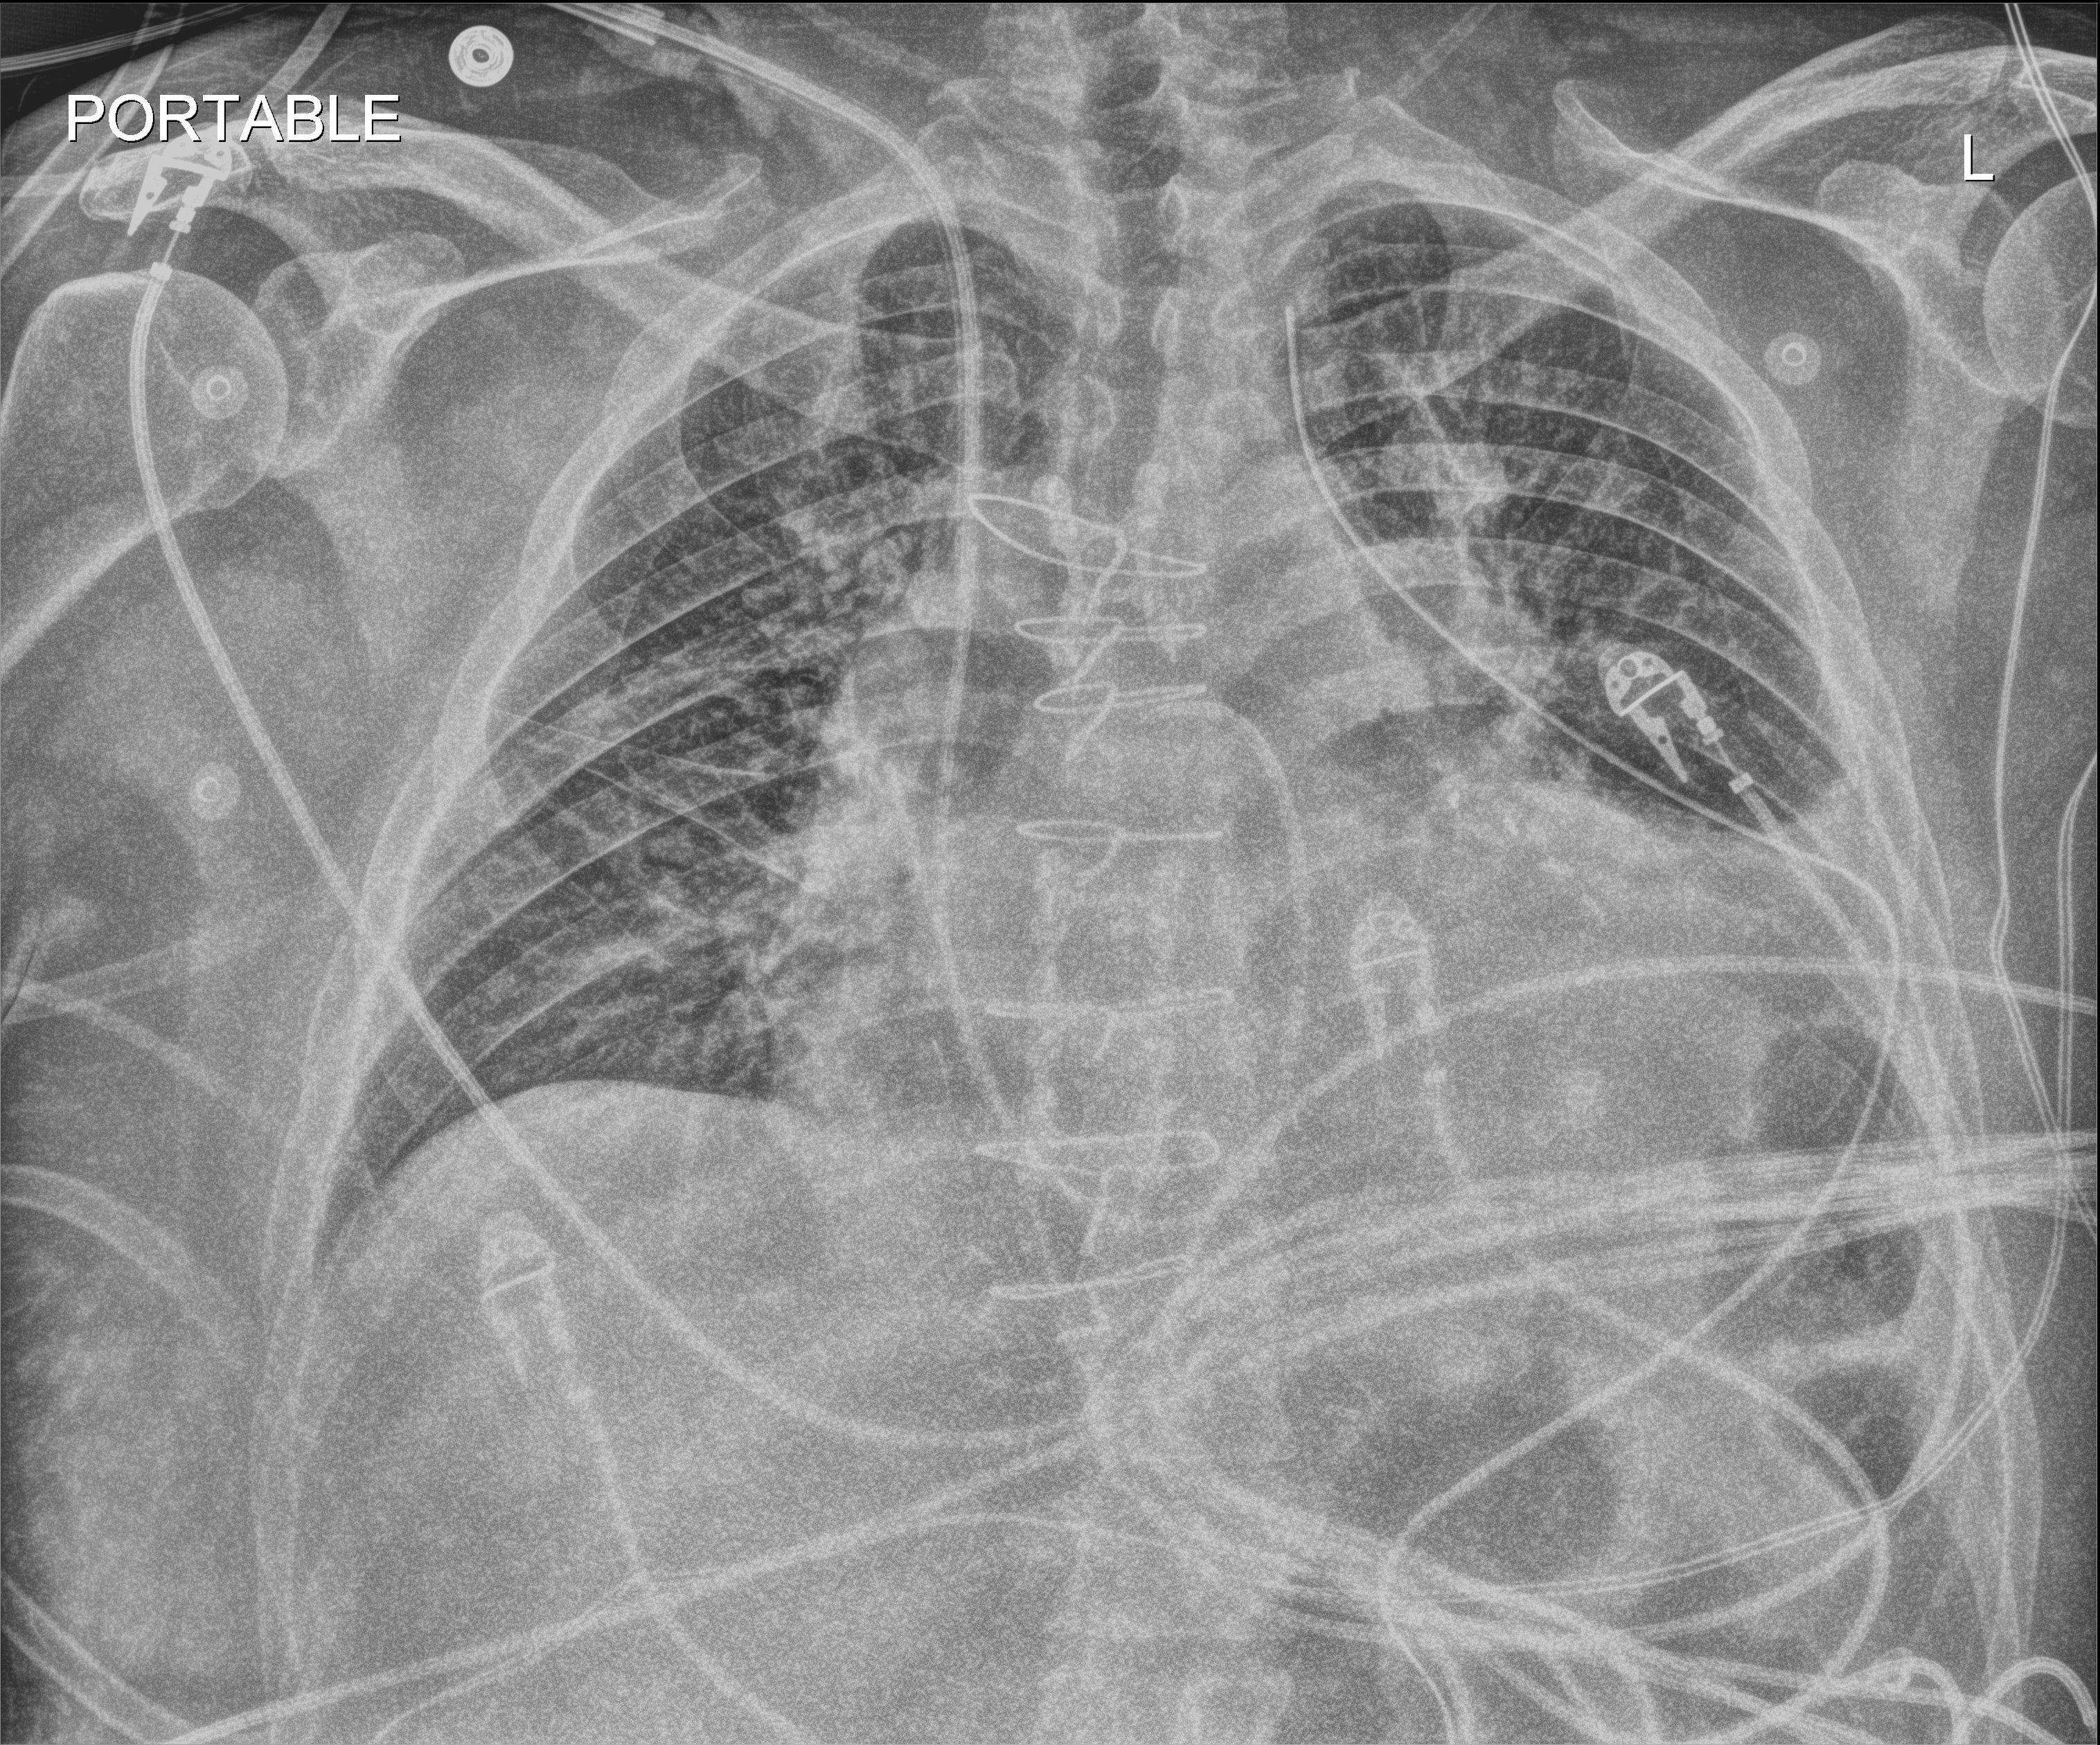
Bedside chest radiograph (digital radiography); anteroposterior (AP) projection. Male patient hospitalised with COVID-19, age 18–59 years.
Hospital-stay facts (about this admission, not read from this image; timing relative to this image not recorded): mechanically ventilated during this hospital stay: no.